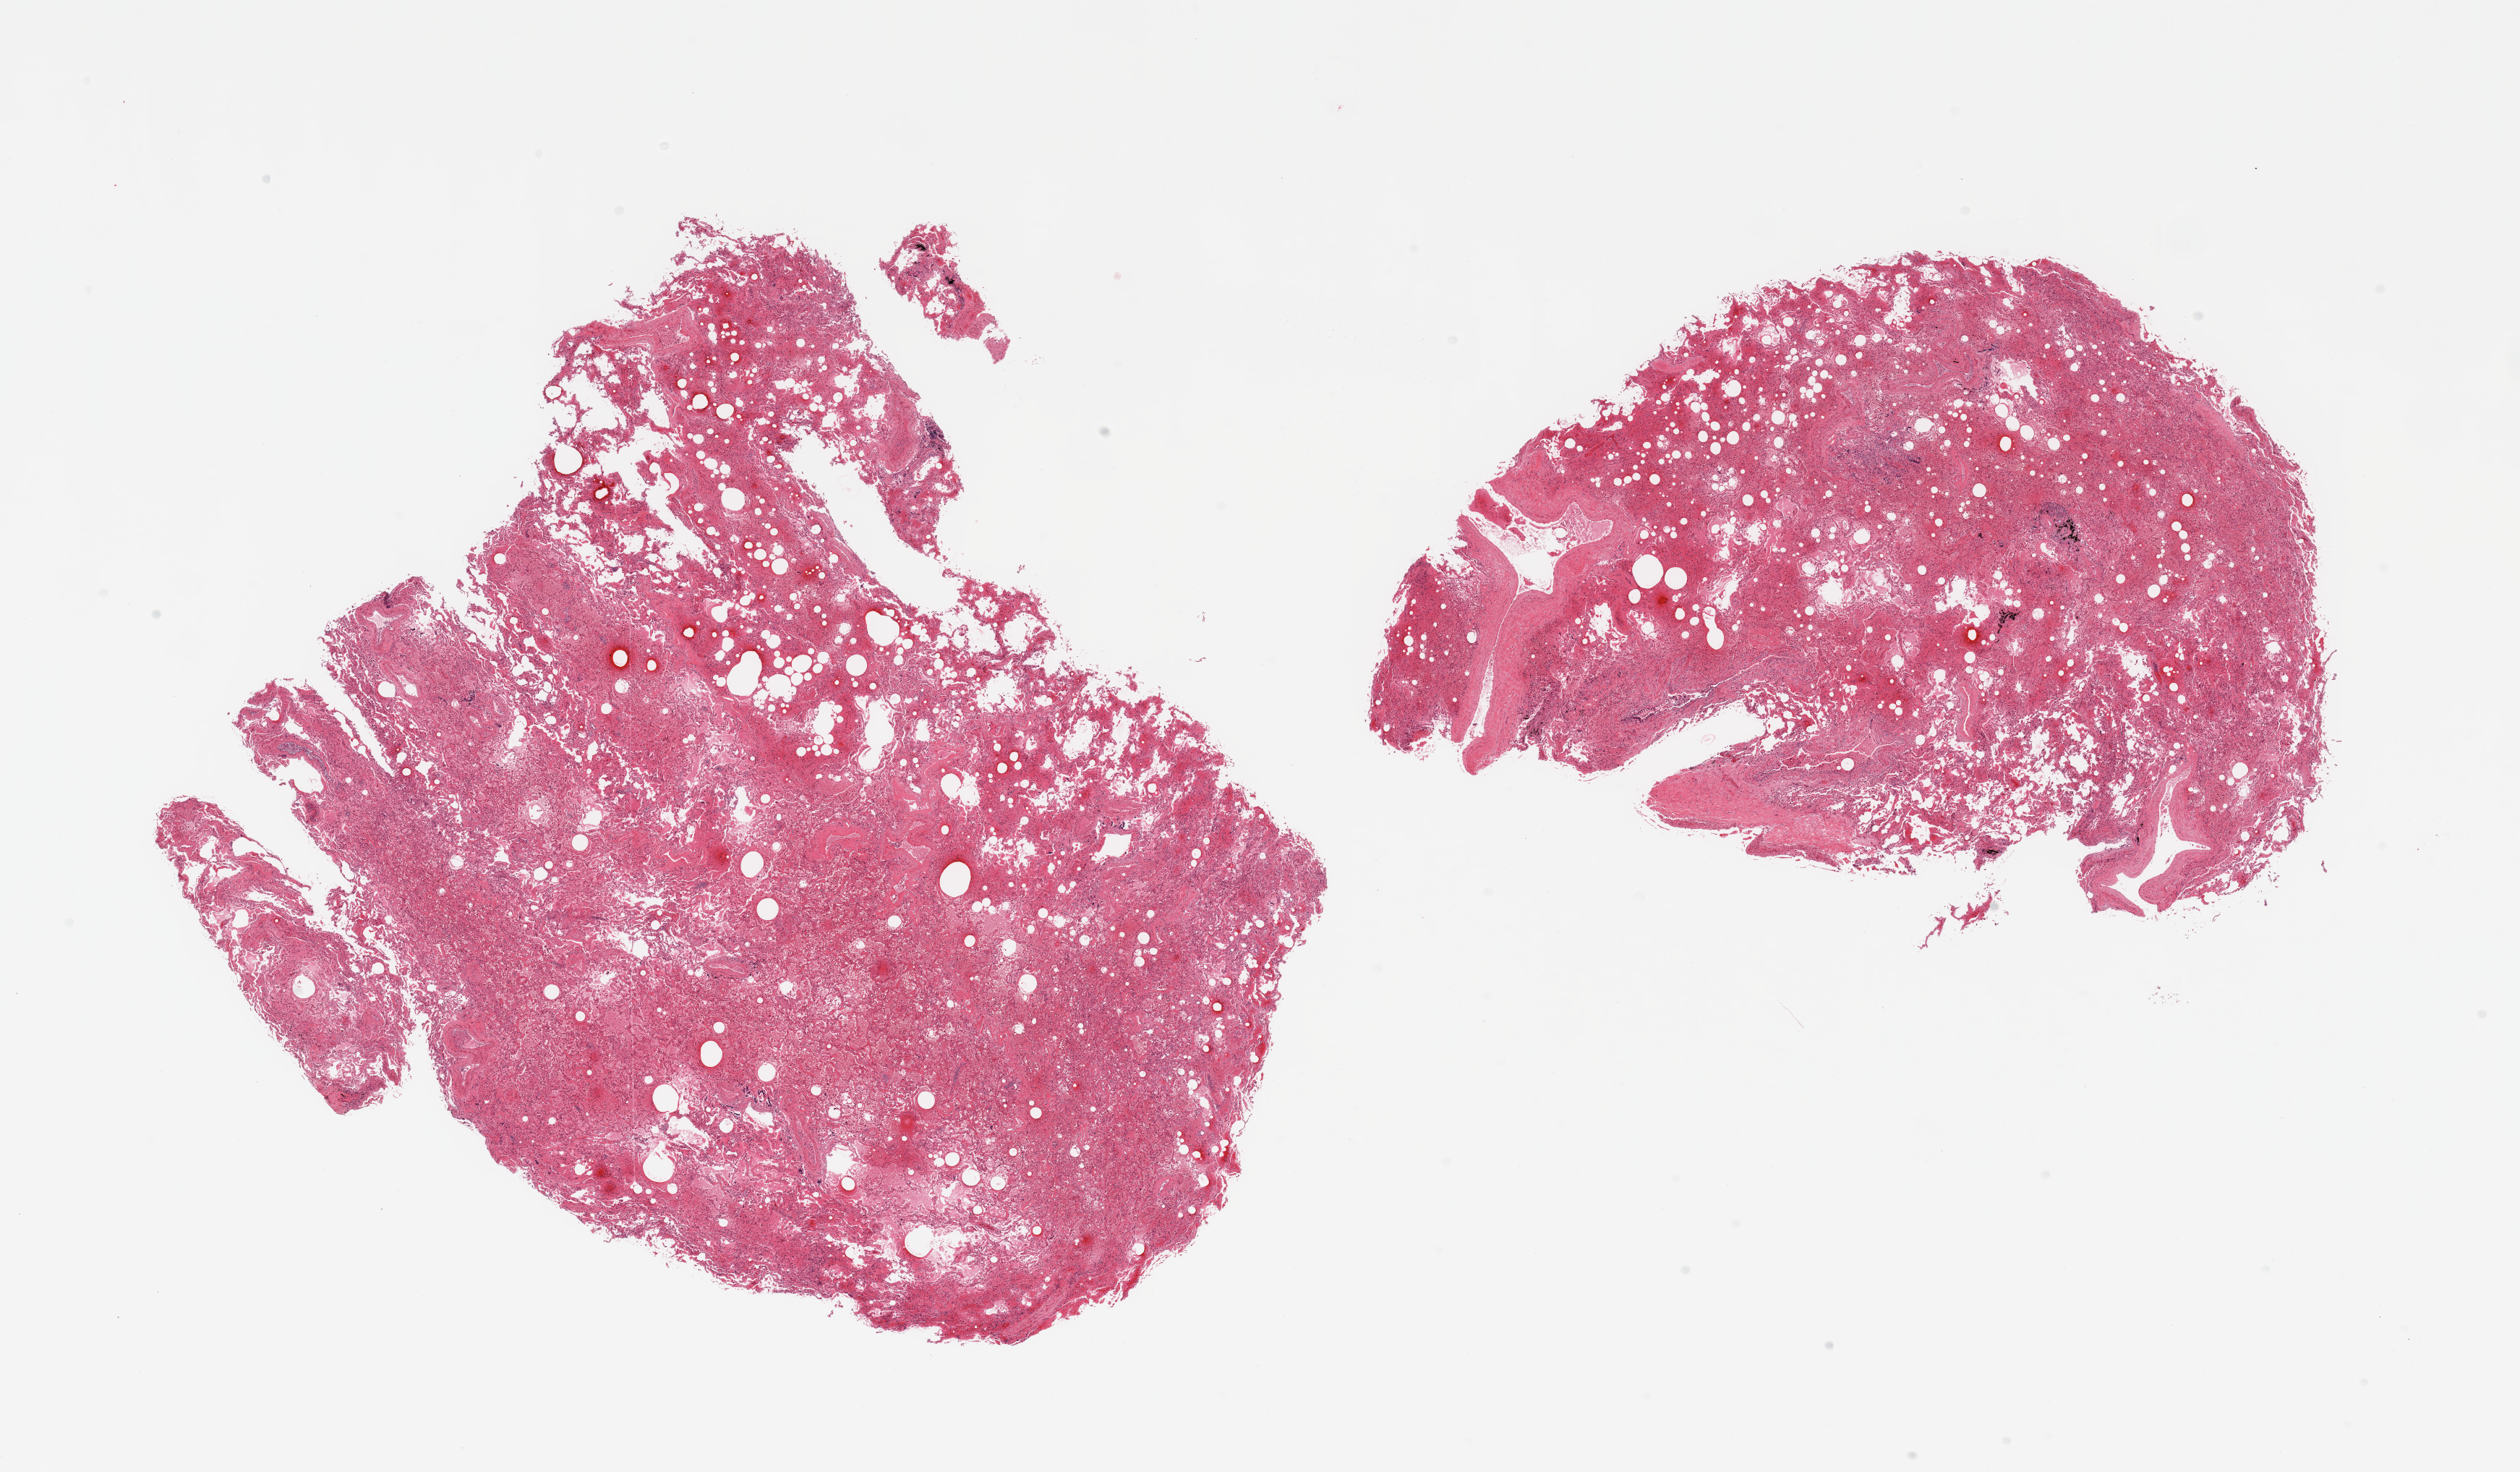
Whole-slide image, haematoxylin and eosin stain, low-resolution overview of the scanned area, about 27.6 x 16.1 mm (from a 20x scan), PAXgene-fixed paraffin-embedded (PFPE) section, target tissue: lung, tissue donor sample.
Pathologist's review note for this sample: 2 pieces; marked congestion, hemosiderinophages, edema and anthracosis.